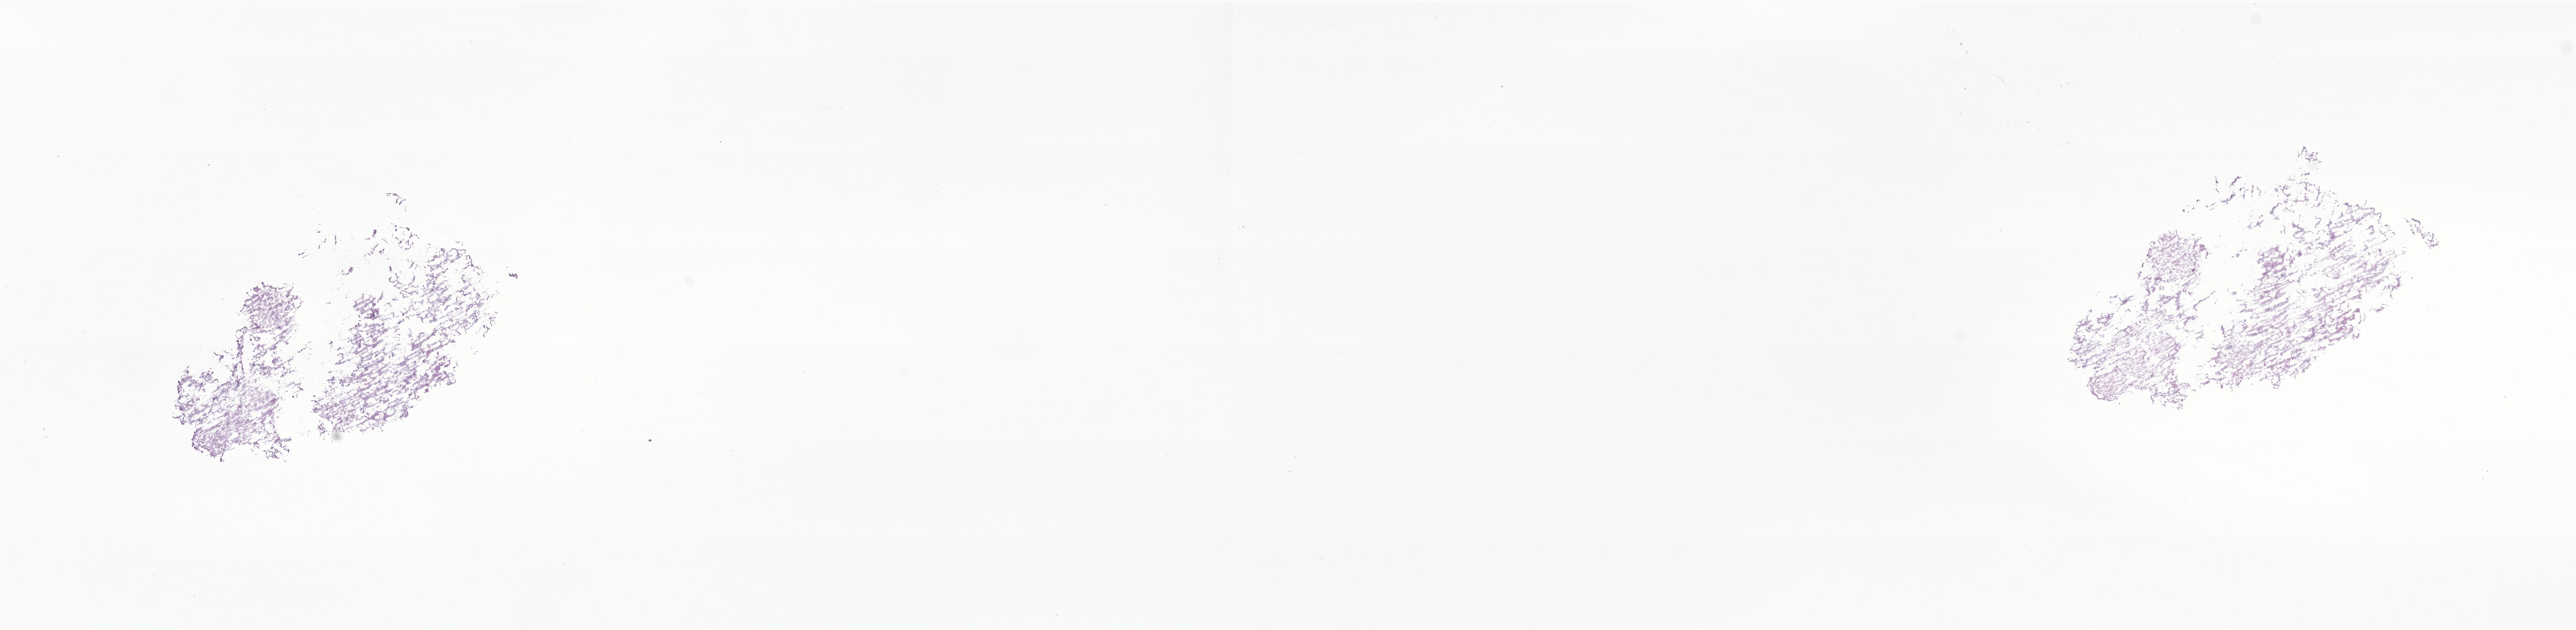
Whole-slide image, haematoxylin and eosin stain of tumor tissue from the cerebellum — a low-resolution overview of the entire scanned area, about 28.5 x 7.0 mm; frozen section. Patient female; age 70 months (5 years 10 months).
• diagnosis (ICD-O-3 morphology term): Pilocytic astrocytoma